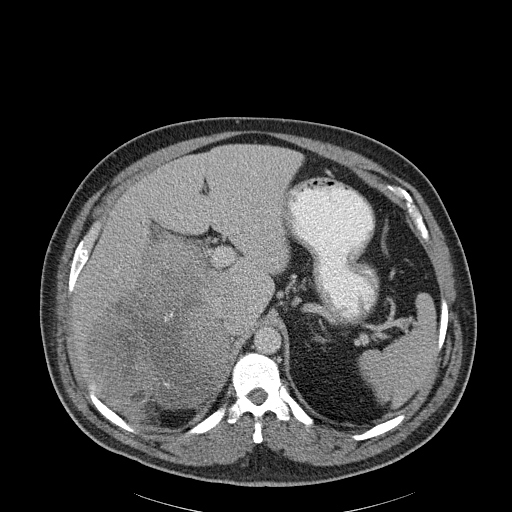
Contrast-enhanced abdominal CT, one axial slice. Reconstruction kernel B30f. 120 kVp. Soft-tissue window (W 400 / L 40 HU). 3 mm slice thickness. 512 × 512 image matrix. Male patient, age 56 years. Case-level facts recorded for this patient, not image findings: diagnosis: adrenocortical carcinoma; tumour side: right adrenal; tumour size at pathology: 18 cm; Ki-67 index: 2 %; stage (as recorded): 3.
Structures marked on this image (semi-automatically segmented with operator editing):
- mass: bounding box <91,246,226,416> (left, top, right, bottom; pixels)